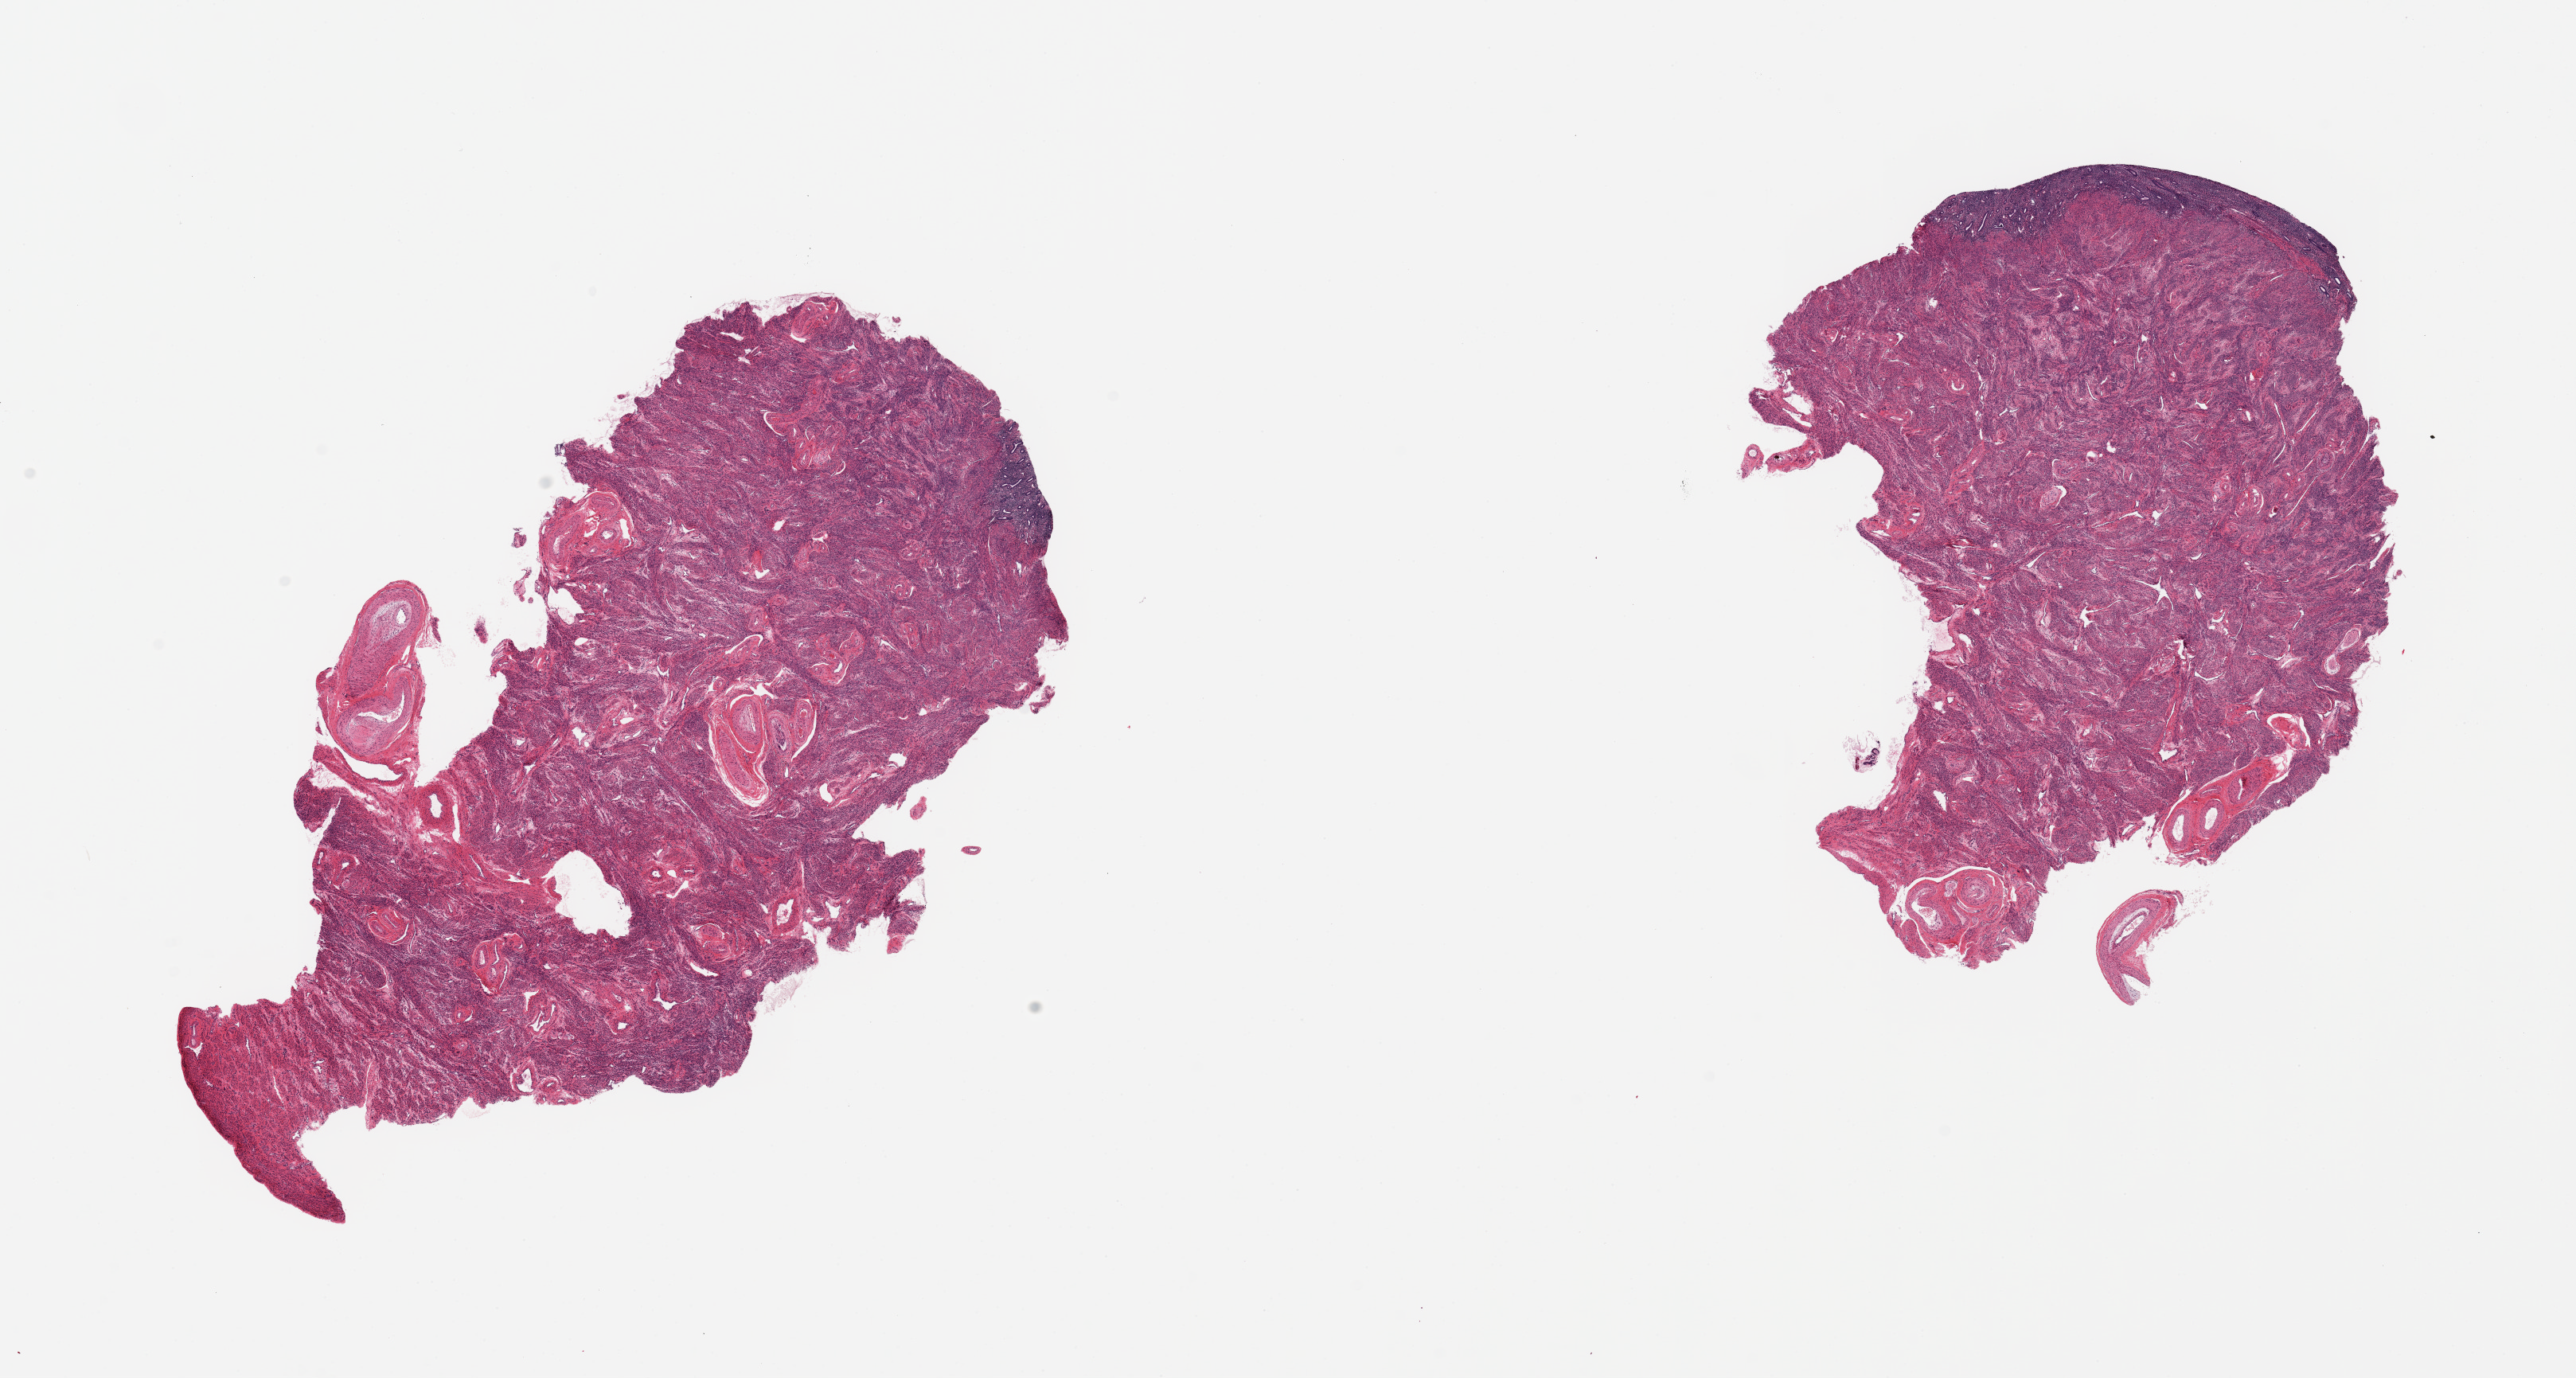
Hematoxylin and eosin (H&E) whole-slide image, brightfield — whole scanned area (about 25.6 x 13.7 mm, slide scanned at 20x) shown as a low-resolution overview, PAXgene-fixed paraffin-embedded (PFPE) section, section of uterus (target tissue), tissue donor sample. Female donor.
- pathologist's review note for this sample: 2 pieces mainly myometrium, thin (~0.5mm) layer of inactive/basalis endometrial glands/stroma